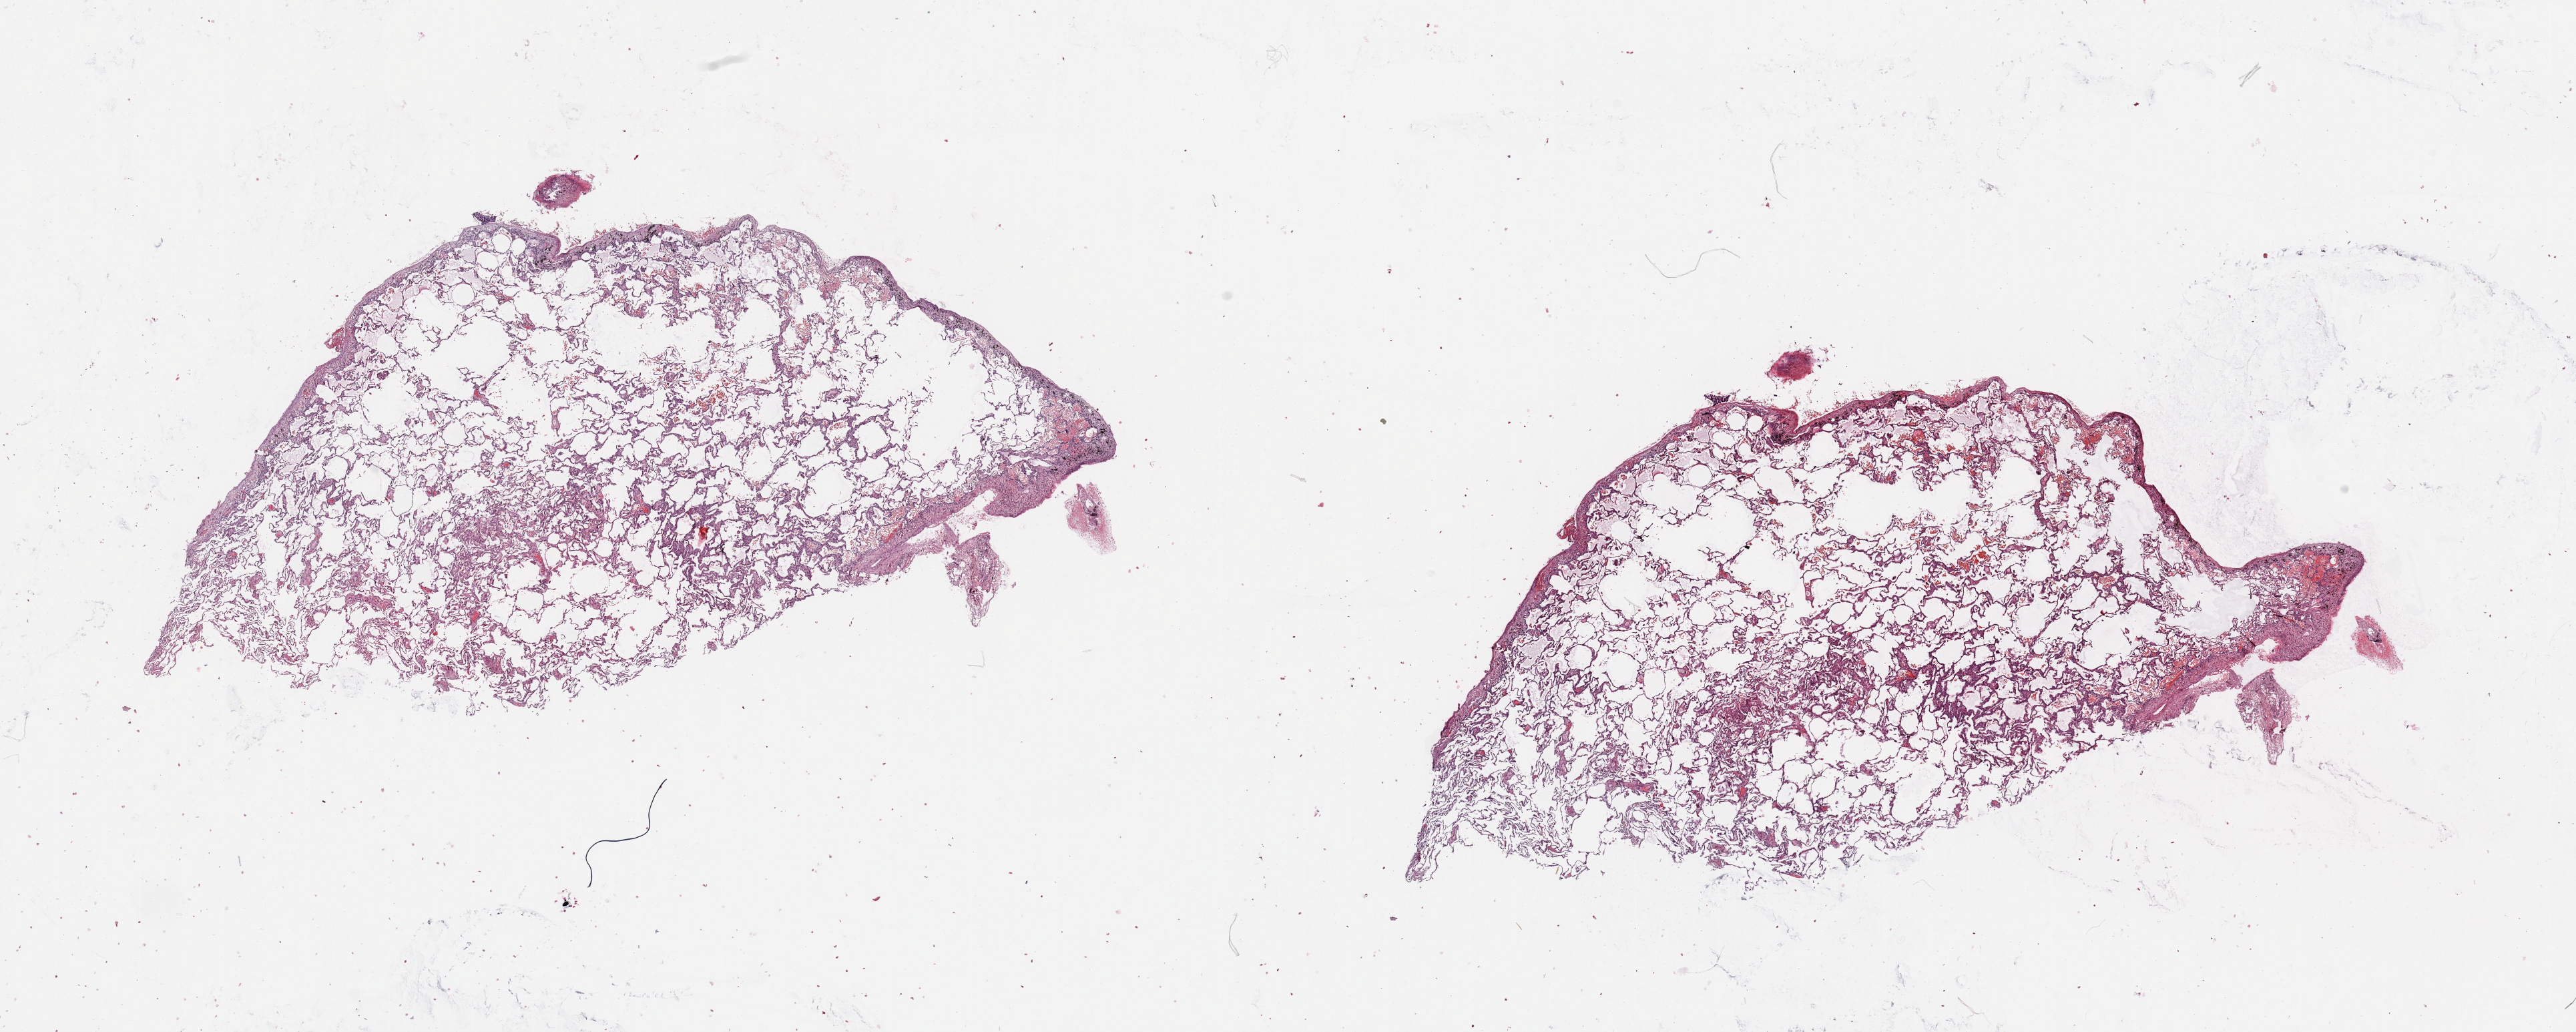
H&E-stained whole-slide image — low-resolution overview of the scanned area, about 30.5 x 12.2 mm (slide scanned at 20x); normal (non-tumour) tissue sample, sampled site: lung. 59-year-old male patient.
- this section: normal (non-tumour) tissue from the same patient
- patient diagnosis: Adenocarcinoma, NOS